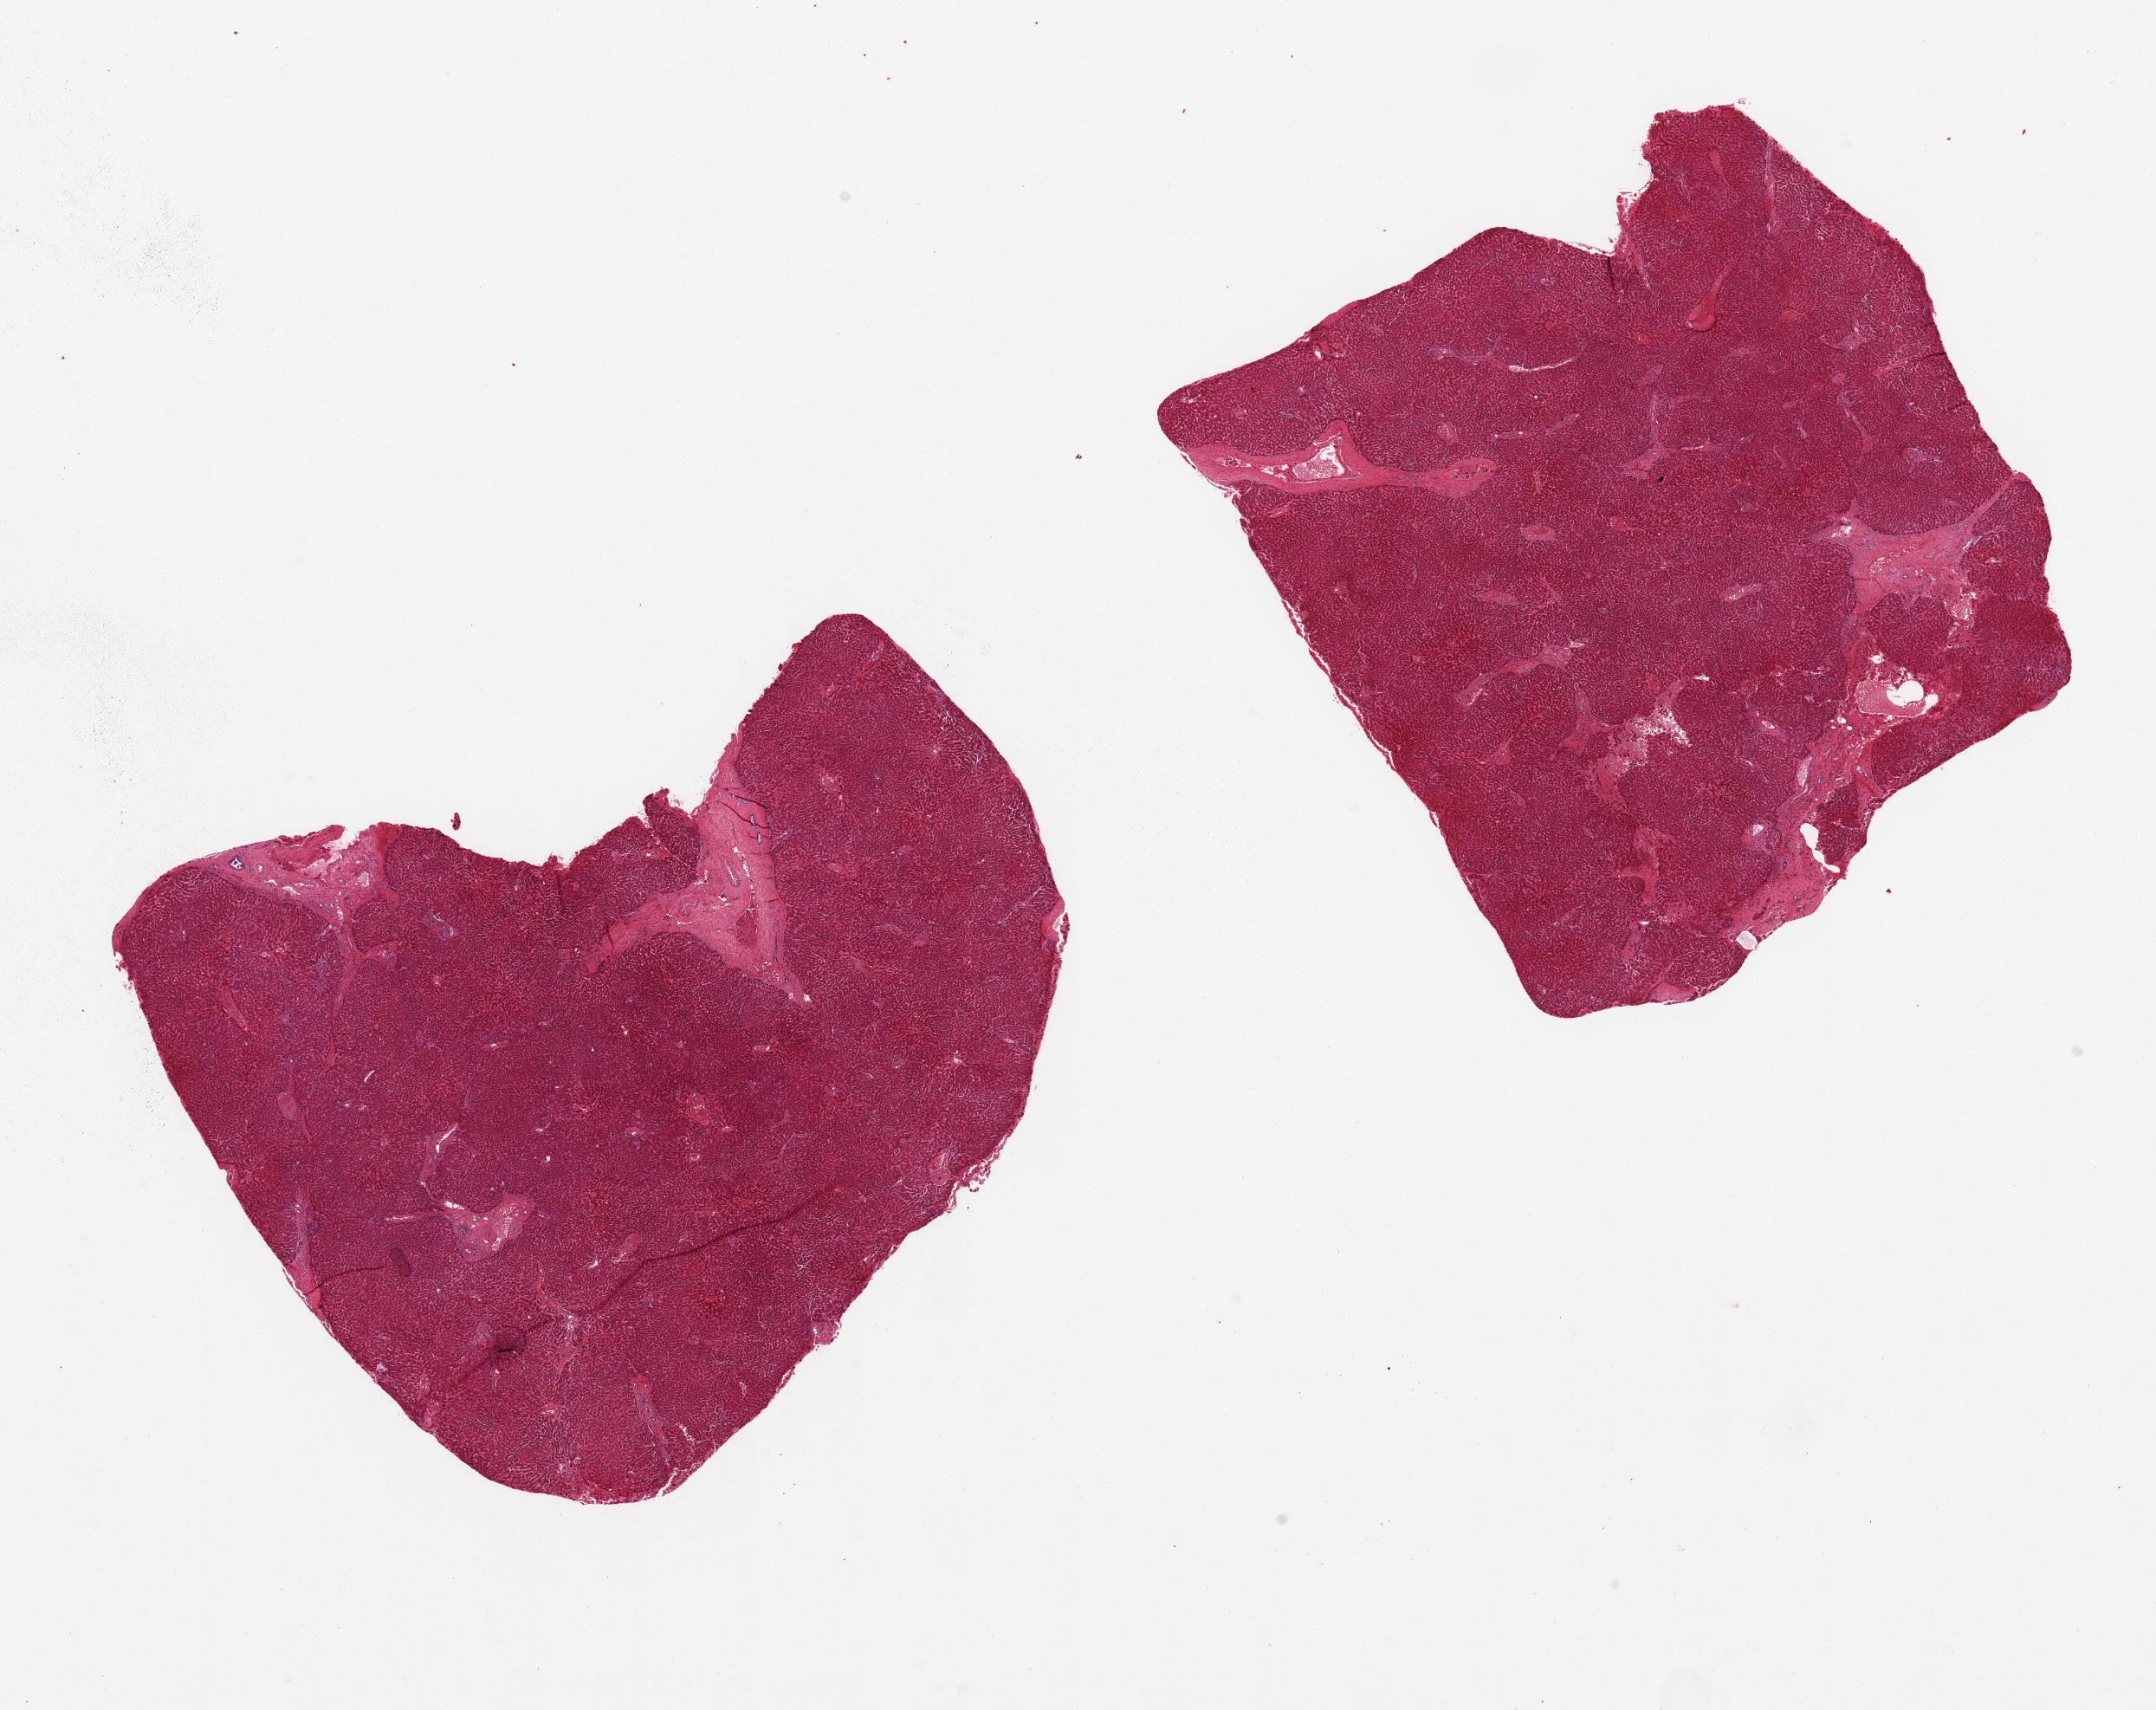
Whole-slide image, H&E stain, low-resolution overview of the scanned area, about 19.7 x 15.6 mm (from a 20x scan), PAXgene-fixed paraffin-embedded (PFPE) section, sampled site (target tissue): liver, tissue donor sample. Donor: male.
Pathologist's review note for this sample: 2 pieces, 8x7 & 7x6 mm; no congestion.